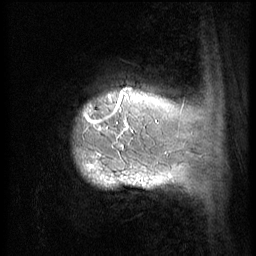
Breast MRI (dynamic contrast-enhanced), one sagittal slice. Position 7 of 56 along the scan axis. 3 images stored at this slice position (order not interpretable as contrast timing). 1.5 T. TE 4.2 ms, TR 9 ms. 2.5 mm slice thickness. 256 × 256 image matrix, field of view 180 × 180 mm. Patient: female, 49 years. From the clinical record (not read from this slice): setting: breast cancer imaged before/during neoadjuvant chemotherapy; receptor status: HER2-positive.
Structures marked on this image (semi-automatic segmentation, software-assisted and operator-edited):
- analysis volume of interest (the breast-tissue region the enhancement analysis was run in; not a lesion): bounding box <60,79,152,203> (left, top, right, bottom; pixels)
- tumour enhancement mask (voxels above the 140 % enhancement threshold inside the analysis volume of interest): <84,87,146,188>